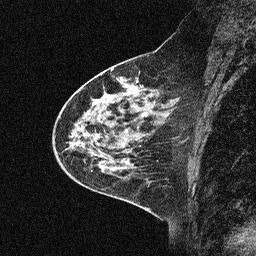
Breast MRI (dynamic contrast-enhanced), one sagittal slice. Position 23 of 64 along the scan axis. Dynamic contrast-enhanced study with each time point stored as its own series, time point 2 of 3 at this slice position (early post-contrast, ordered by acquisition time). 1.5 T. TE 4.5 ms, TR 11 ms. 256 × 256 image matrix, field of view 200 × 200 mm. Patient: female, 46 years. Case-level facts recorded for this patient, not image findings: setting: breast cancer imaged before/during neoadjuvant chemotherapy; receptor status: HER2-positive.
Outlined on this slice (semi-automatically segmented with operator editing):
- analysis volume of interest (the breast-tissue region the enhancement analysis was run in; not a lesion): bounding box [x1, y1, x2, y2] px = [46, 51, 180, 169]
- tumour enhancement mask (voxels above the 90 % enhancement threshold inside the analysis volume of interest): [91, 81, 137, 167]